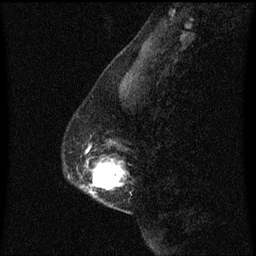
Breast MRI (dynamic contrast-enhanced), one sagittal slice. Dynamic contrast-enhanced series, image 2 of 3 at this slice position (ordered by acquisition). 1.5 T. TE 4.2 ms, TR 8.4 ms. 256 × 256 image matrix, field of view 200 × 200 mm. Patient: female, 40 years. From the clinical record (not read from this slice): setting: breast cancer imaged before/during neoadjuvant chemotherapy; receptor status: triple-negative.
Structures marked on this image (semi-automatically segmented with operator editing):
- analysis volume of interest (the breast-tissue region the enhancement analysis was run in; not a lesion): box from (x=70, y=142) to (x=127, y=213) px
- tumour enhancement mask (voxels above the 70 % enhancement threshold inside the analysis volume of interest): (x=90, y=160)–(x=125, y=195)